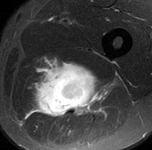
MRI of an extremity soft-tissue mass, one axial slice. Position 80 of 90 along the scan axis. STIR. MR volume resampled by the dataset authors to the PET/CT grid (not the native acquisition matrix). 152 × 150 image matrix, field of view 148 × 146 mm. Male patient. Case-level facts recorded for this patient, not image findings: histological type: undifferentiated pleomorphic liposarcoma; grade: high; site of the primary tumour: left thigh.
Structures marked on this image (expert contour drawn on MRI and transferred to this co-registered scan by the dataset authors):
- gross tumour volume including surrounding oedema: bounding box <27,60,110,122> (left, top, right, bottom; pixels)
- gross tumour volume (mass): <32,62,101,118>